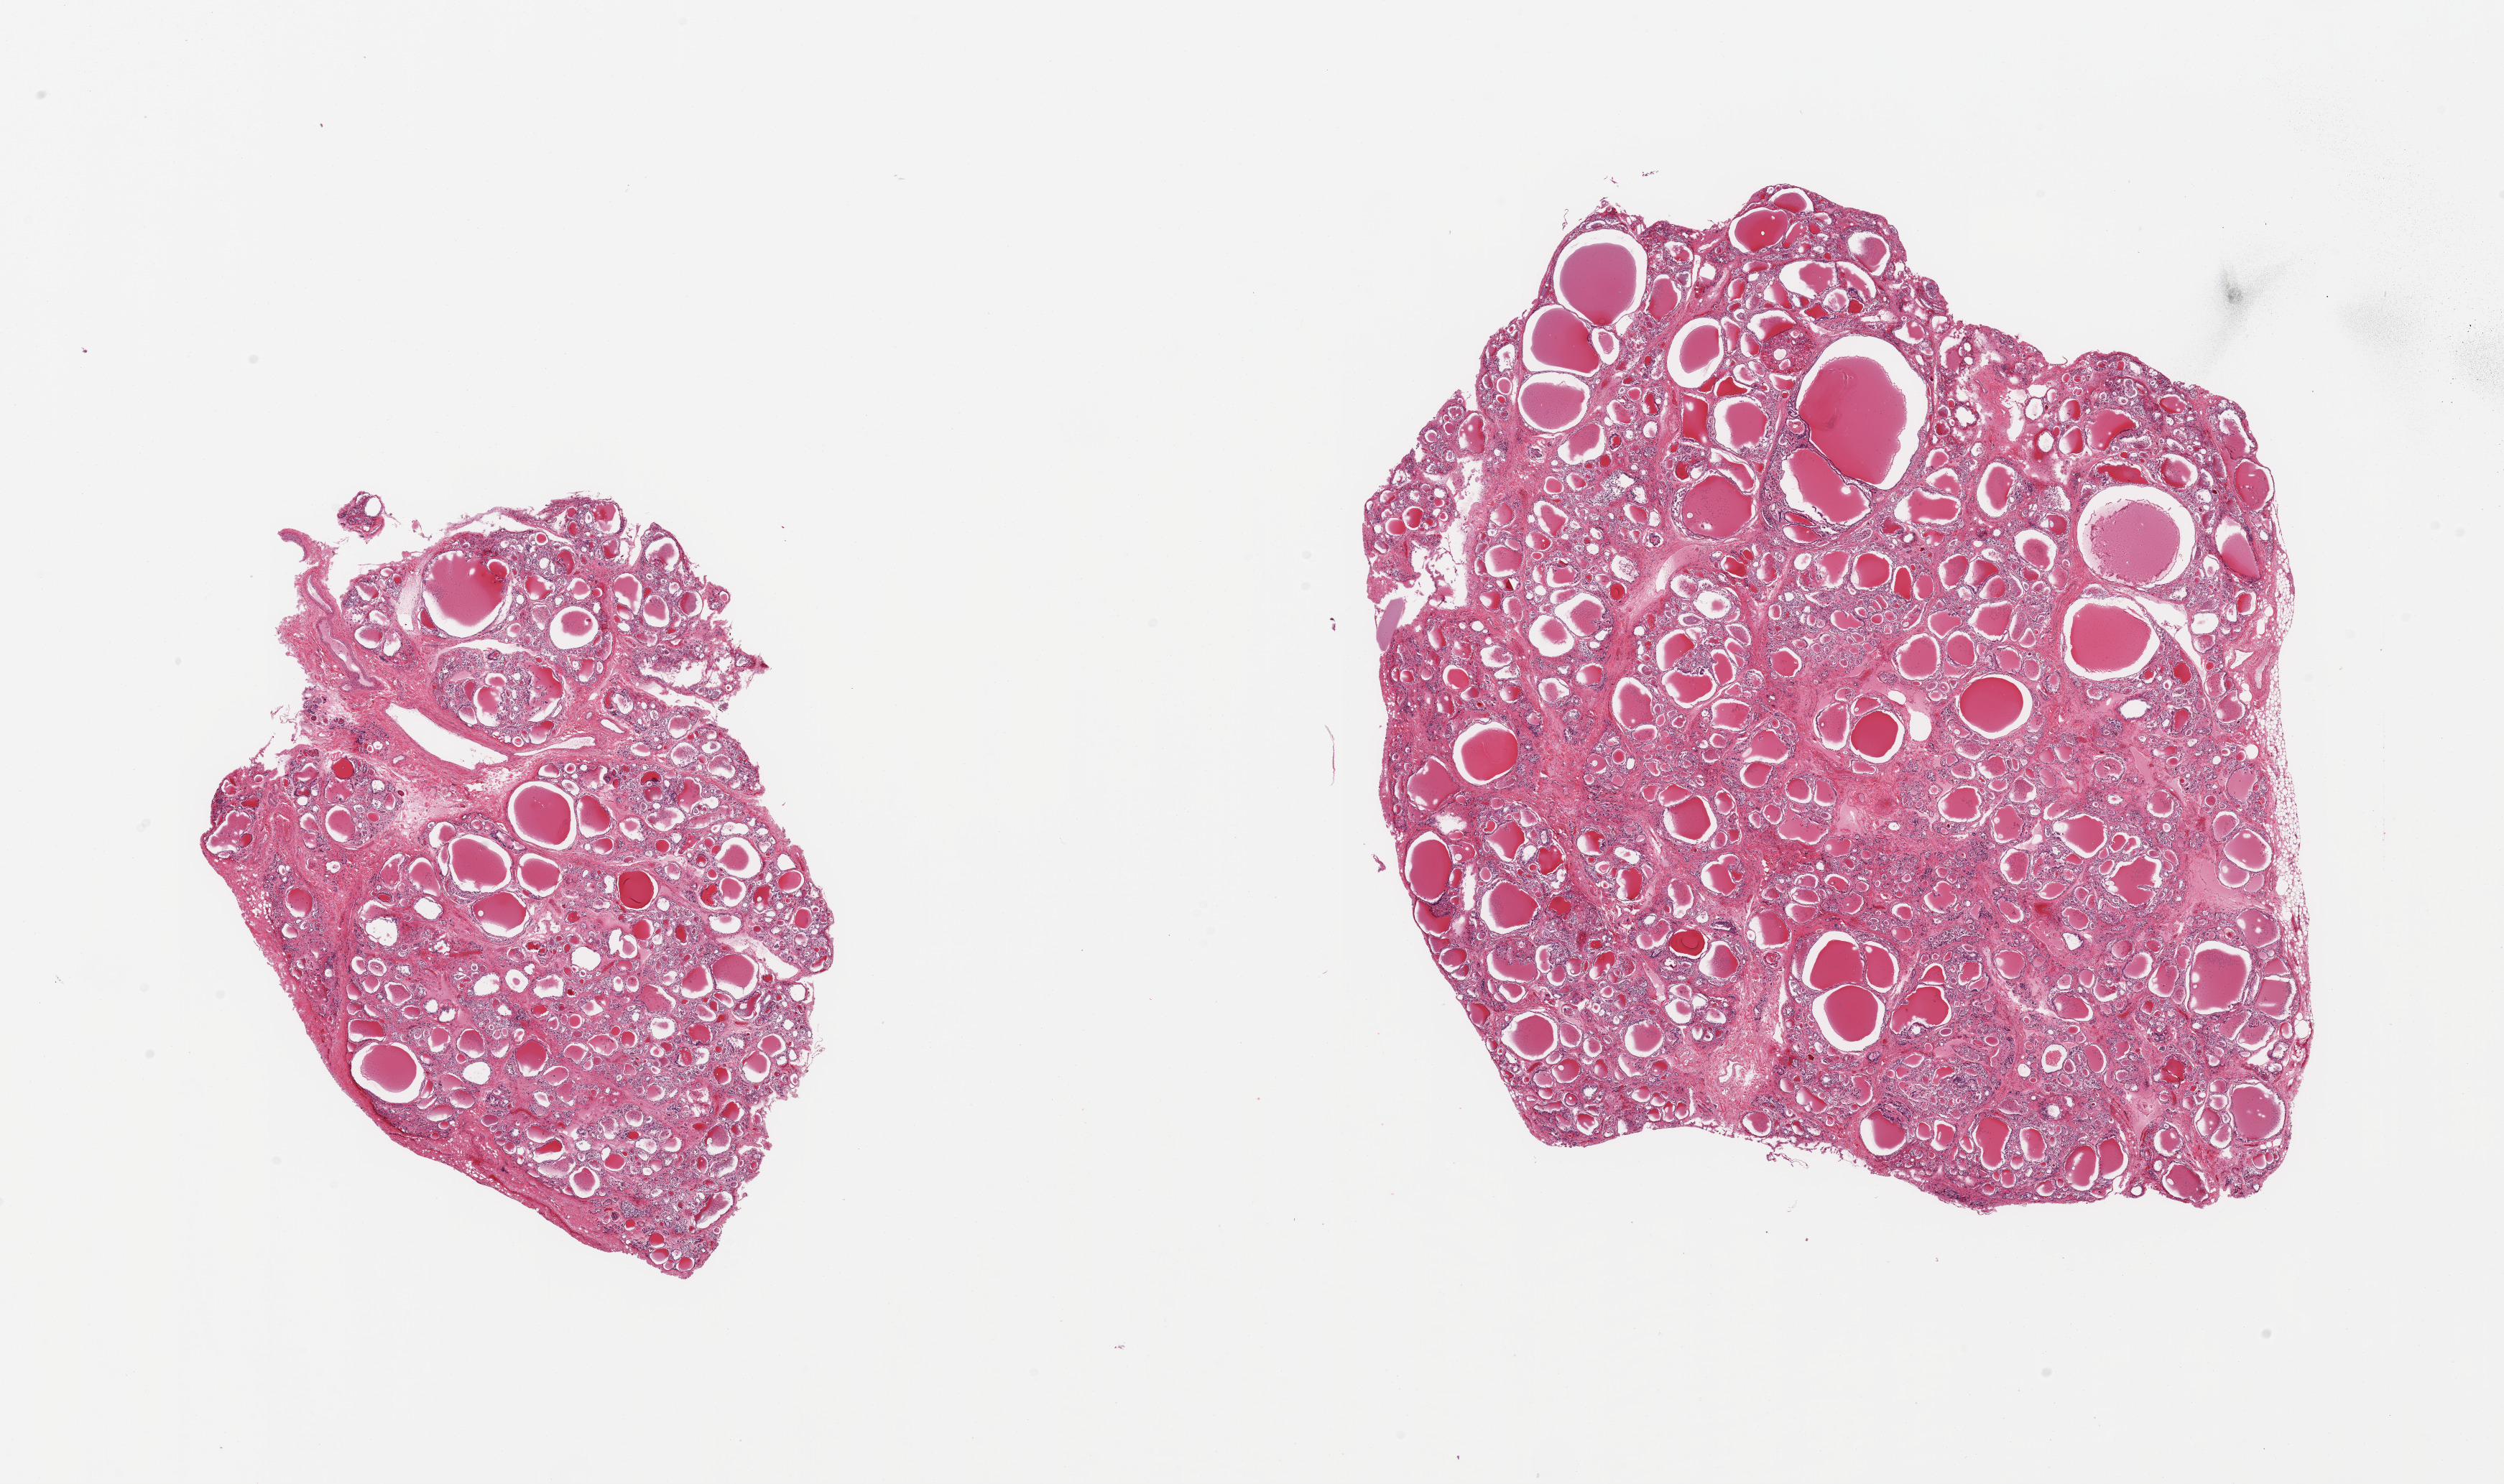
H&E whole-slide image, shown as a low-resolution overview of the whole scanned area (about 27.6 x 16.3 mm, from a 20x scan); PAXgene-fixed paraffin-embedded (PFPE) section; sampled site (target tissue): thyroid; donor tissue sample.
Pathologist's review note for this sample: 2 pieces; interstitial fibrosis and micronodularity (differently sized follicles surrounded by fibrous tissue).